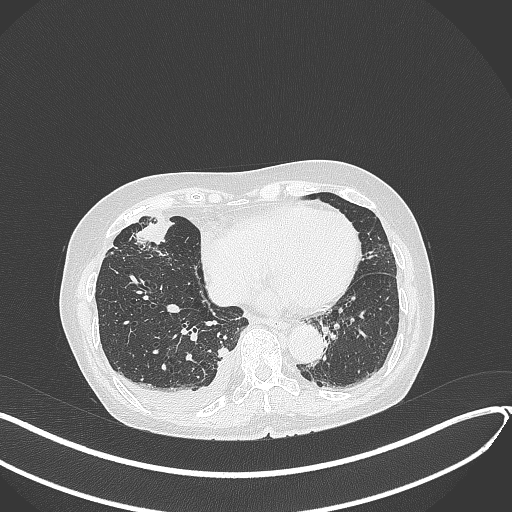
Chest CT, one axial slice. Slice 125 of 418 in the series (ordered by position). Reconstruction kernel B70f. 120 kVp. Lung window (W 1500 / L -600 HU). 512 × 512 image matrix, field of view 400 × 400 mm. Female patient, age 75 years. Case-level facts recorded for this patient, not image findings: clinical TNM (as recorded): T2a N3 M0.
Structures marked on this image (rectangle marked by the reading radiologist):
- lung tumour (recorded histology: adenocarcinoma): bounding box <131,213,179,251> (left, top, right, bottom; pixels)